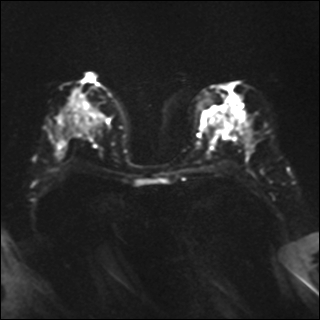
Breast MRI, one axial slice. Slice 18 of 35 in the series (ordered by position). Diffusion-weighted series; image 2 of 4 stored at this slice position (different b-values; order by instance number). 1.5 T. 4 mm slice thickness. 320 × 320 image matrix, field of view 320 × 320 mm. Female patient.
Outlined on this slice (manually delineated by an expert):
- tumour on diffusion-weighted imaging: bounding box (x1, y1, x2, y2) in pixels: (212, 118, 215, 121)